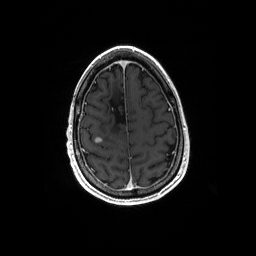
Brain MRI from a brain-tumour surgery series, one axial slice; slice 45 of 192 in the series (ordered by position); T1-weighted post-contrast; 256 × 256 image matrix, field of view 256 × 256 mm. Case-level facts recorded for this patient, not image findings: histopathology: Astrocytoma; WHO grade: 4; IDH mutation: yes.
Structures marked on this image (expert manual segmentation):
- tumour: box from (x=95, y=137) to (x=102, y=144) px